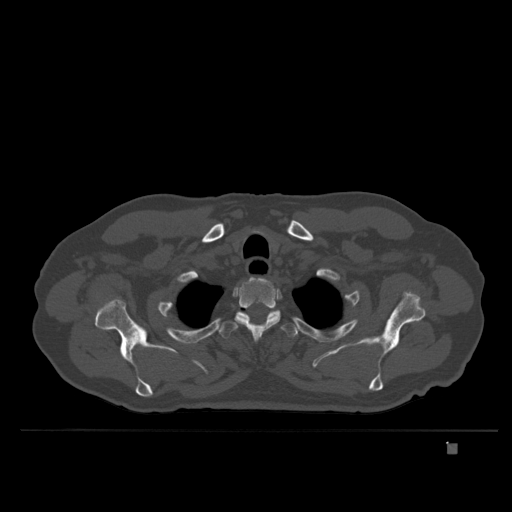
CT including the spine, one axial slice; position 309 of 435 along the scan axis; bone window (W 1800 / L 400 HU); 1.5 mm slice thickness; 512 × 512 image matrix, field of view 434 × 434 mm. Male patient, age 73 years. Case-level facts recorded for this patient, not image findings: primary cancer: skin.
Structures marked on this image (semi-automatic segmentation, software-assisted and operator-edited):
- T2 vertebra: box from (x=235, y=277) to (x=281, y=338) px
- T3 vertebra: (x=219, y=310)–(x=298, y=339)